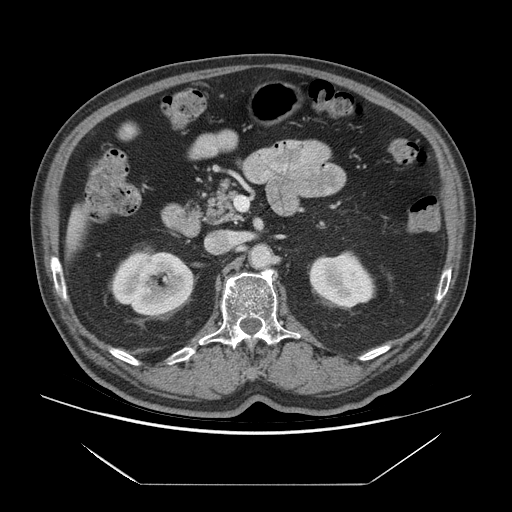
Contrast-enhanced abdominal CT (liver protocol), one axial slice; slice 24 of 75 in the series (ordered by position); 140 kVp; soft-tissue window (W 400 / L 40 HU); 2.5 mm slice thickness; 512 × 512 image matrix. From the clinical record (not read from this slice): diagnosis: hepatocellular carcinoma (patient treated with transarterial chemoembolisation; whether this scan precedes or follows treatment is not stated here); TNM stage (as recorded): Stage-I; Child-Pugh class: A; tumour differentiation: well differentiated; tumour nodularity: uninodular.
Annotated regions visible in this slice (semi-automatic segmentation, software-assisted and operator-edited):
- liver parenchyma outside the tumour (the mass and vessels are separate outlines, so this box may not span the whole liver): bounding box (x1, y1, x2, y2) in pixels: (66, 207, 84, 254)